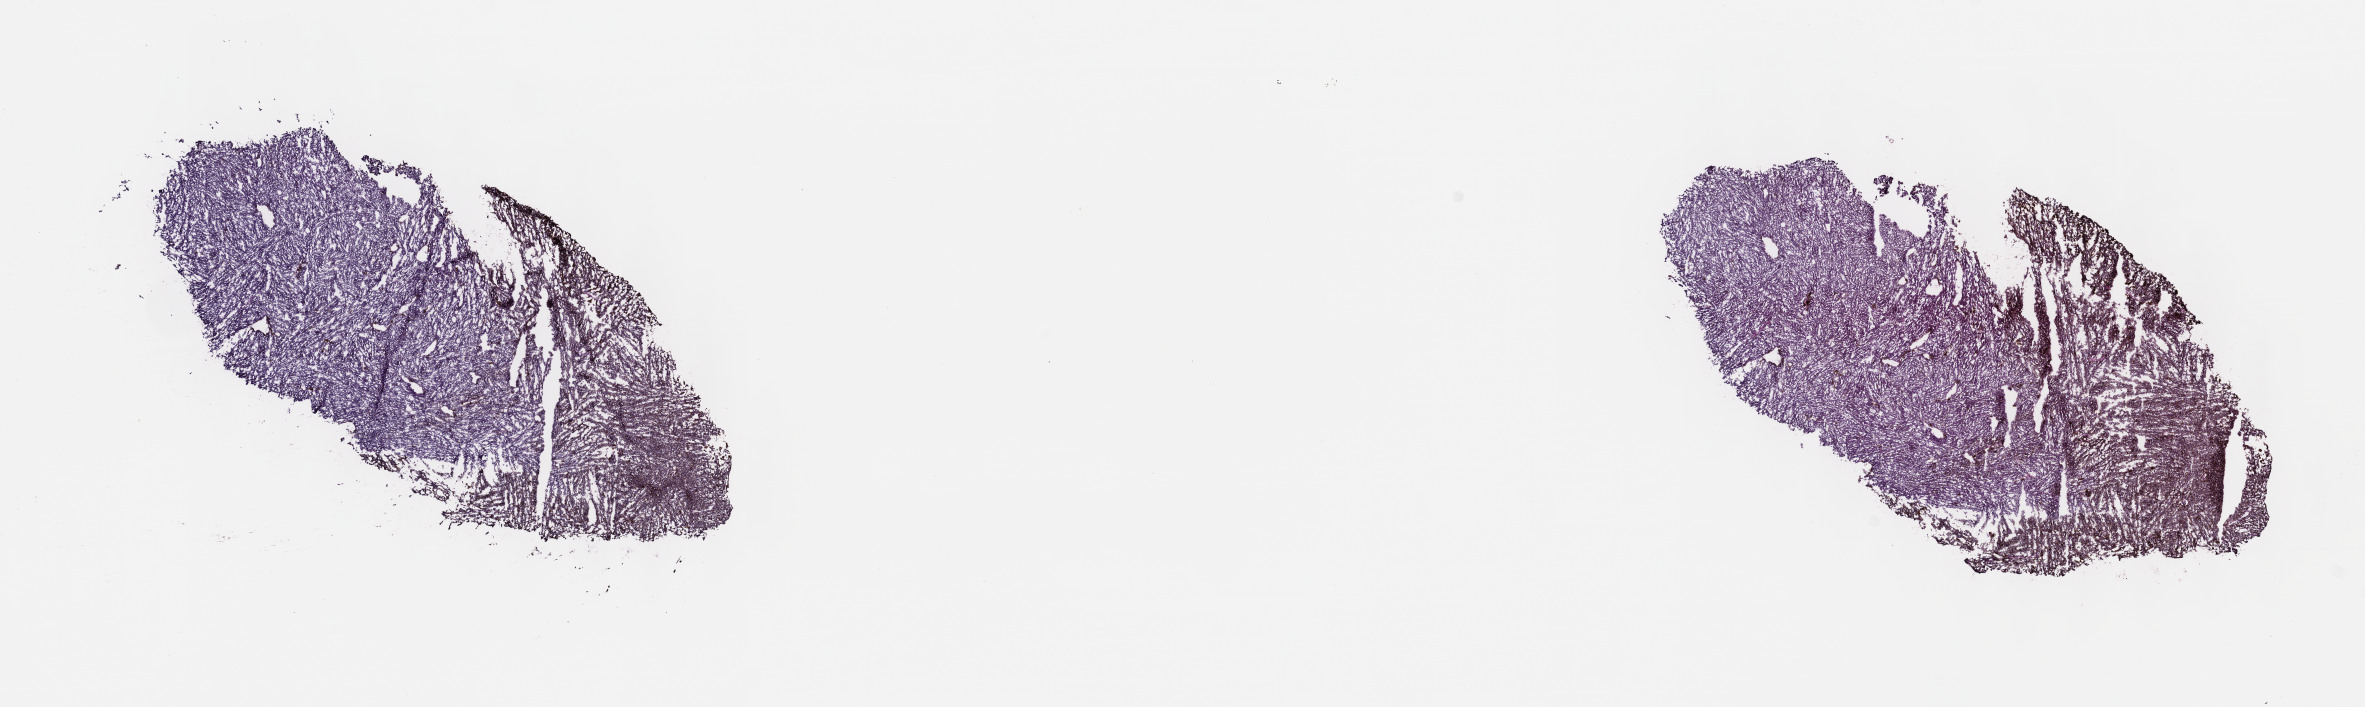
H&E-stained whole-slide image — low-resolution overview of the scanned area, about 19.1 x 5.7 mm (slide scanned at 40x), frozen section from the top of the tissue portion, sample: primary tumour, uvea. Patient: male, age at initial diagnosis 60 years. Pathologist review of this section (percent, as recorded): tumour cells 85%, tumour nuclei 85%.
Pathologic diagnosis: Spindle cell melanoma, NOS (choroid).